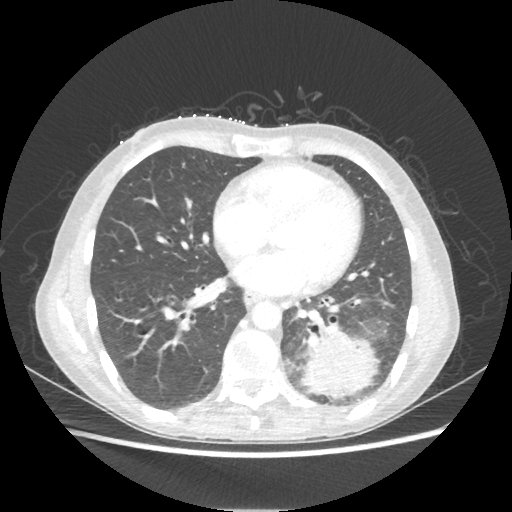
Chest CT, one axial slice. Position 91 of 221 along the scan axis. Reconstruction kernel STANDARD. Lung window (W 1500 / L -600 HU). 1.25 mm slice thickness. 512 × 512 image matrix. Female patient, age 53 years. Case-level facts recorded for this patient, not image findings: clinical TNM (as recorded): T3 N0 M0.
Structures marked on this image (bounding box drawn by a radiologist):
- lung tumour (recorded histology: adenocarcinoma): bounding box (x1, y1, x2, y2) in pixels: (304, 326, 377, 398)